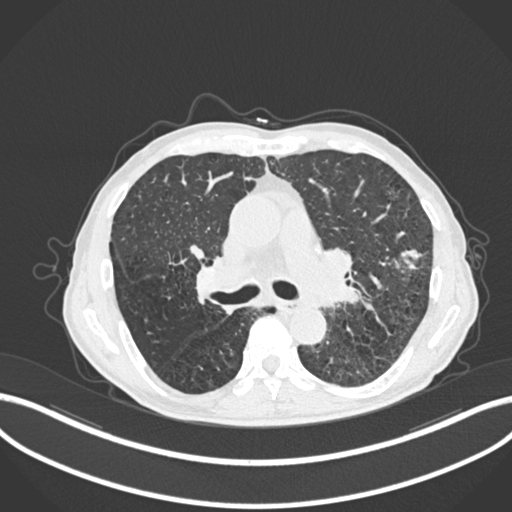
Chest CT, one axial slice. Position 152 of 287 along the scan axis. Reconstruction kernel B30f. 120 kVp. Lung window (W 1500 / L -600 HU). 1 mm slice thickness. 512 × 512 image matrix, field of view 400 × 400 mm. Male patient, age 74 years. Case-level facts recorded for this patient, not image findings: clinical TNM (as recorded): T2a N1 M0.
Outlined on this slice (bounding box drawn by a radiologist):
- lung tumour (recorded histology: adenocarcinoma): bounding box (x1, y1, x2, y2) in pixels: (398, 246, 423, 275)